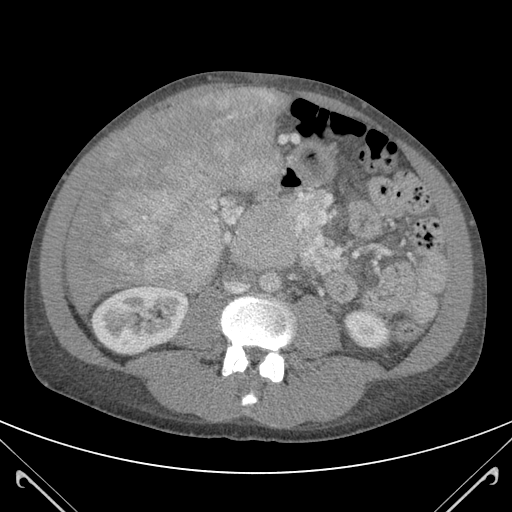
Contrast-enhanced abdominal CT (liver protocol), one axial slice. Position 42 of 118 along the scan axis. 120 kVp. Soft-tissue window (W 400 / L 40 HU). 3 mm slice thickness. 512 × 512 image matrix. Case-level facts recorded for this patient, not image findings: diagnosis: hepatocellular carcinoma (patient treated with transarterial chemoembolisation; whether this scan precedes or follows treatment is not stated here); TNM stage (as recorded): Stage-IIIB; Child-Pugh class: A; tumour nodularity: uninodular.
Annotated regions visible in this slice (semi-automatically segmented with operator editing):
- liver parenchyma outside the tumour (the mass and vessels are separate outlines, so this box may not span the whole liver): bounding box [x1, y1, x2, y2] px = [66, 88, 283, 311]
- mass: [92, 88, 281, 282]